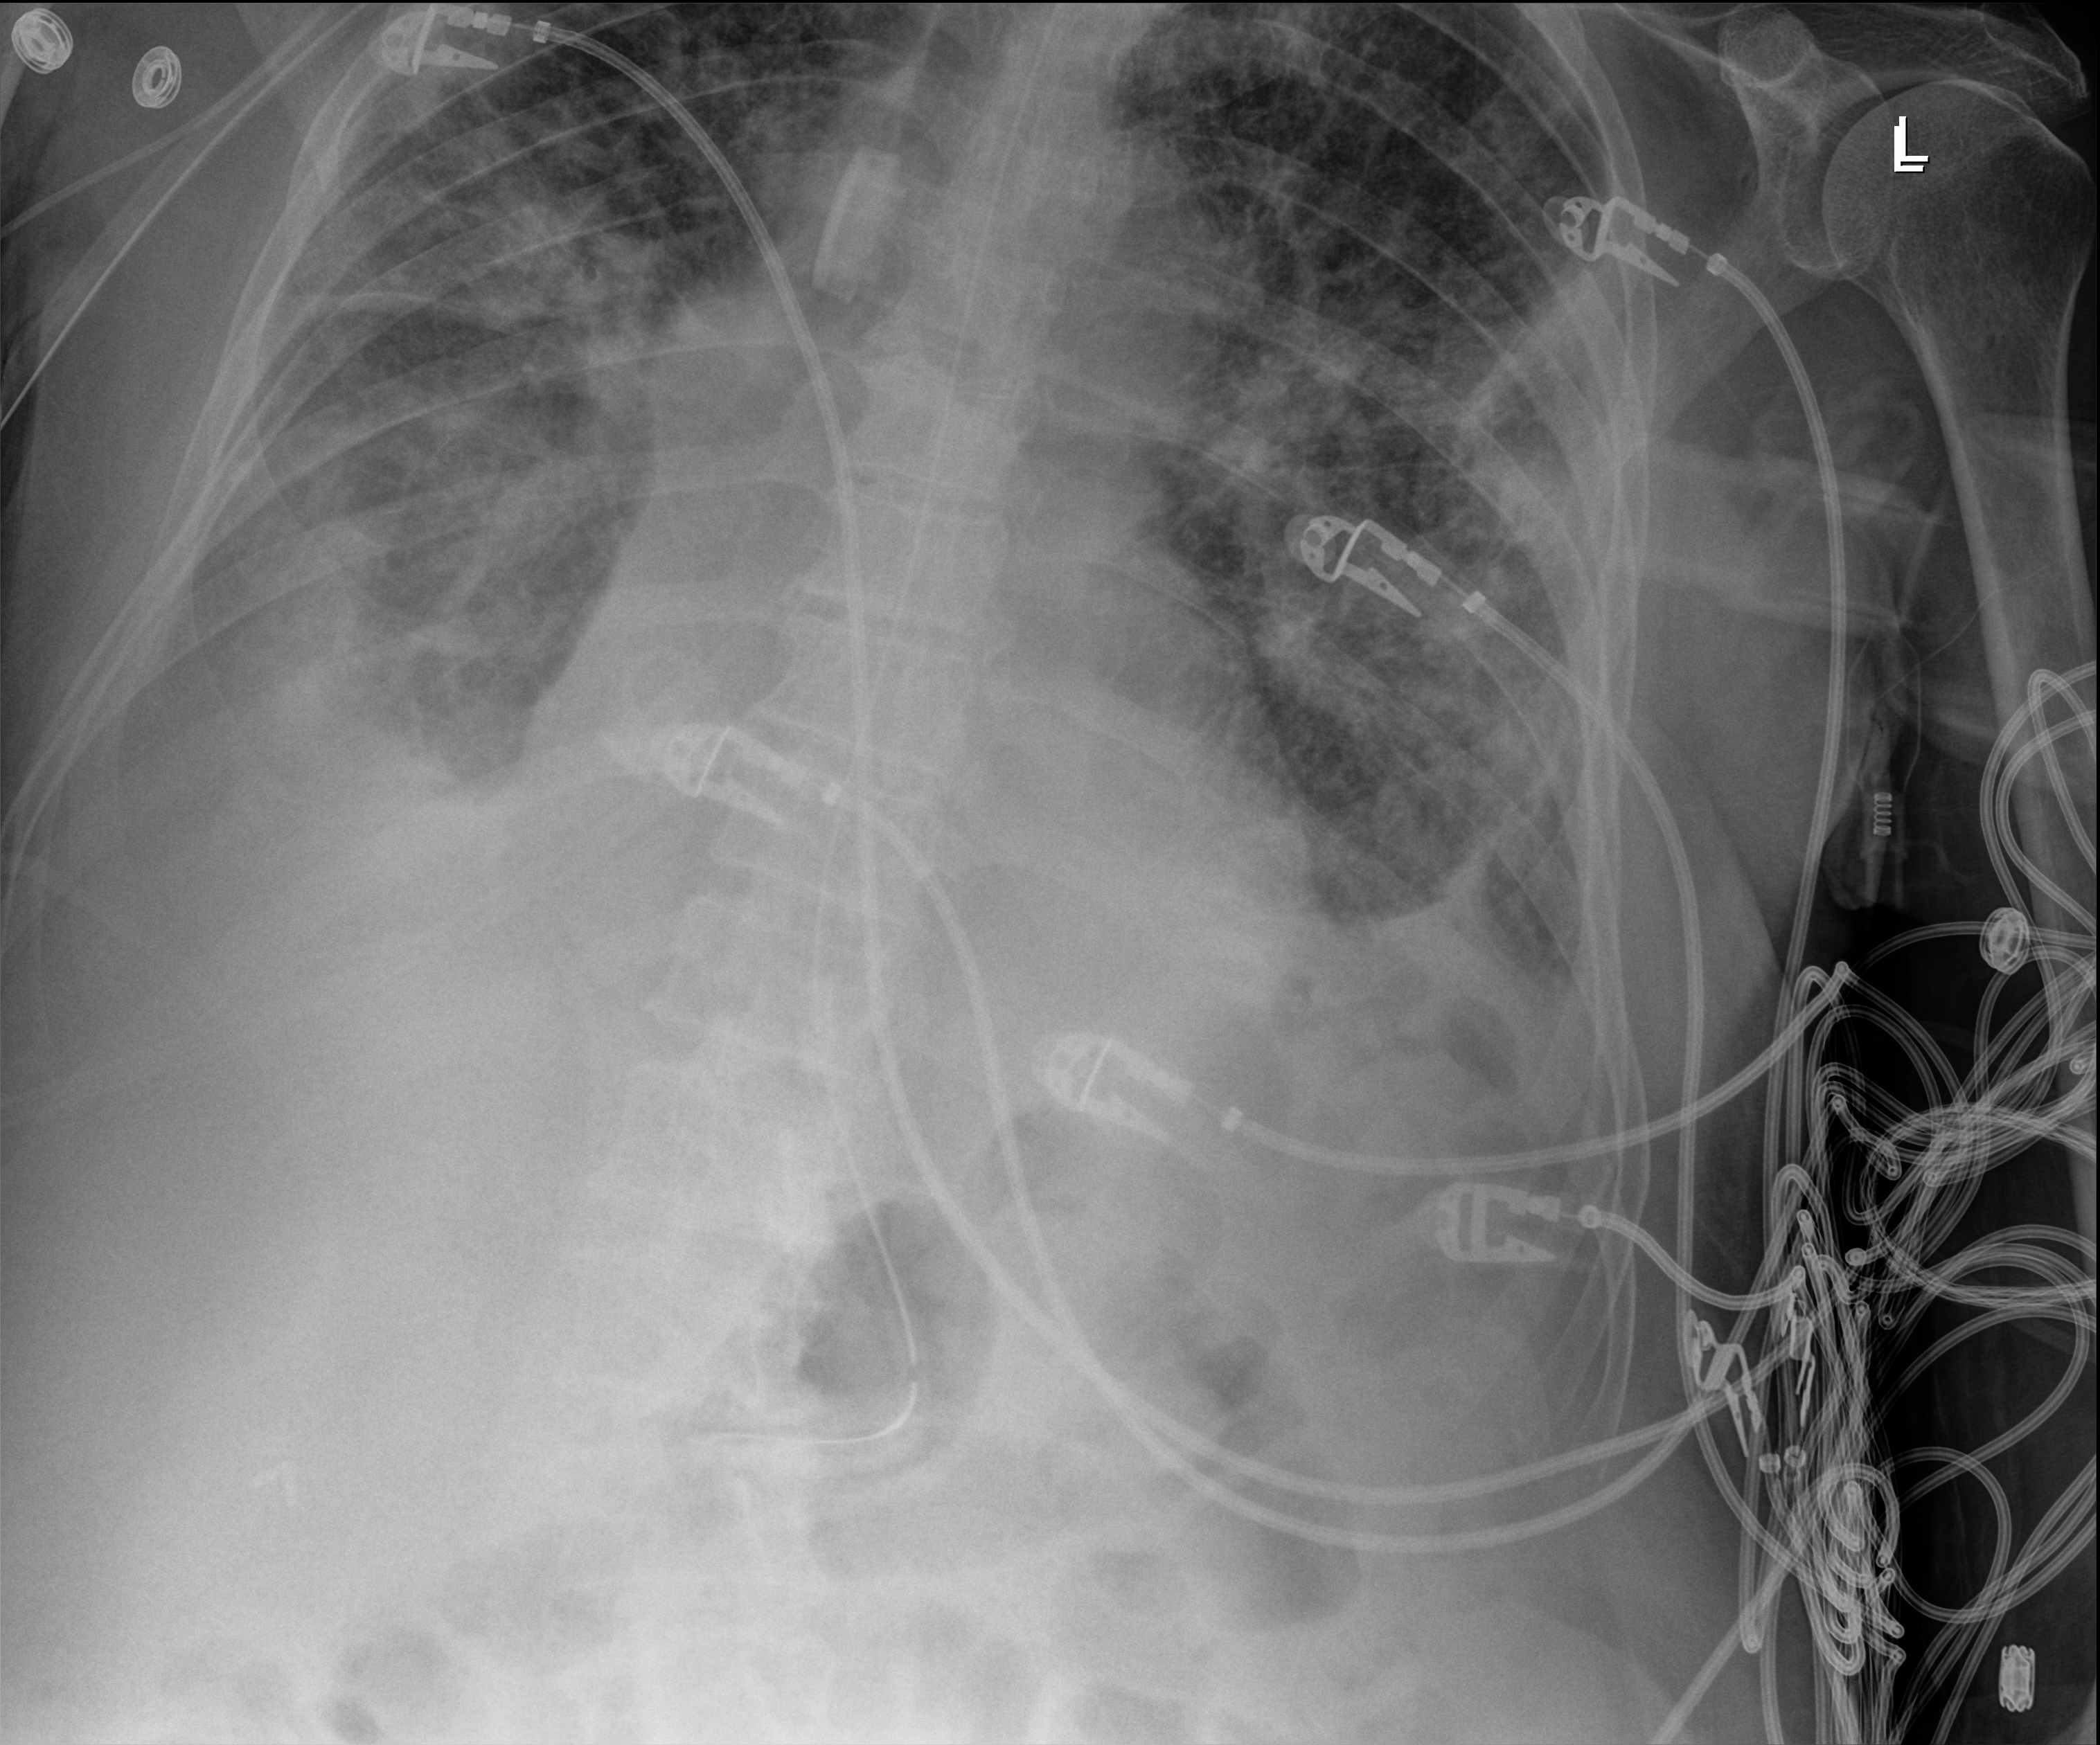
Bedside chest radiograph (digital radiography), anteroposterior (AP) projection. Patient hospitalised with COVID-19; male, aged 75–90 years.
Admission-level facts for this patient (not findings on this image; timing relative to this image not recorded):
- other chronic lung disease (admission record): yes
- admitted to intensive care during this hospital stay: yes